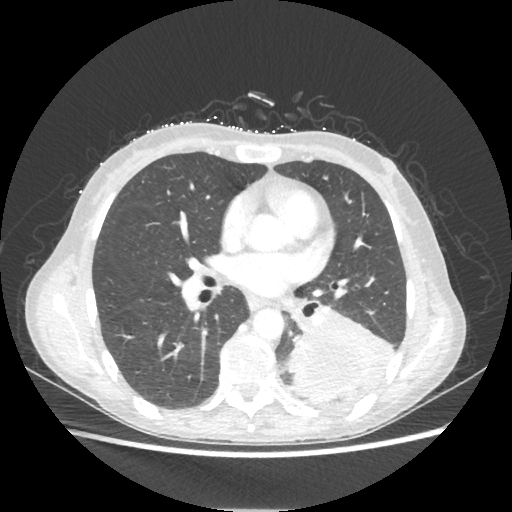
Chest CT, one axial slice; slice 109 of 221 in the series (ordered by position); reconstruction kernel STANDARD; 80 kVp; lung window (W 1500 / L -600 HU); 1.25 mm slice thickness; 512 × 512 image matrix, field of view 360 × 360 mm. Patient: female, 53 years. Case-level facts recorded for this patient, not image findings: clinical TNM (as recorded): T3 N0 M0.
Annotated regions visible in this slice (bounding box drawn by a radiologist):
- lung tumour (recorded histology: adenocarcinoma): bounding box (x1, y1, x2, y2) in pixels: (283, 311, 396, 403)